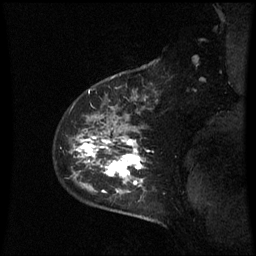
Breast MRI (dynamic contrast-enhanced), one sagittal slice; slice 48 of 60 in the series (ordered by position); dynamic contrast-enhanced series, image 2 of 3 at this slice position (ordered by acquisition); 1.5 T; TE 4.2 ms, TR 8.9 ms; 2.3 mm slice thickness; 256 × 256 image matrix, field of view 210 × 210 mm. Patient: female, 43 years. Case-level facts recorded for this patient, not image findings: setting: breast cancer imaged before/during neoadjuvant chemotherapy; receptor status: HER2-positive.
Structures marked on this image (semi-automatically segmented with operator editing):
- analysis volume of interest (the breast-tissue region the enhancement analysis was run in; not a lesion): bounding box <56,80,155,195> (left, top, right, bottom; pixels)
- tumour enhancement mask (voxels above the 70 % enhancement threshold inside the analysis volume of interest): <77,134,145,193>